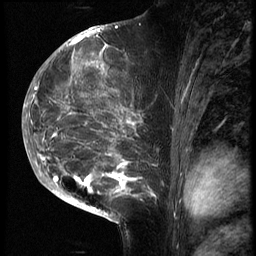
Breast MRI (dynamic contrast-enhanced), one sagittal slice; position 34 of 70 along the scan axis; 3 images stored at this slice position (order not interpretable as contrast timing); 1.5 T; TE 4.2 ms, TR 9 ms; 2.5 mm slice thickness; 256 × 256 image matrix, field of view 180 × 180 mm. Patient: female, 28 years. From the clinical record (not read from this slice): setting: breast cancer imaged before/during neoadjuvant chemotherapy.
Structures marked on this image (semi-automatically segmented with operator editing):
- analysis volume of interest (the breast-tissue region the enhancement analysis was run in; not a lesion): bounding box [x1, y1, x2, y2] px = [43, 42, 167, 215]
- tumour enhancement mask (voxels above the 140 % enhancement threshold inside the analysis volume of interest): [43, 42, 158, 205]